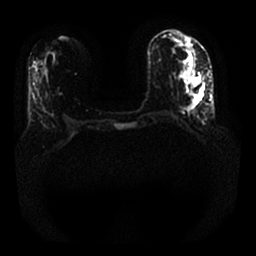
Breast MRI, one axial slice. Position 6 of 25 along the scan axis. Diffusion-weighted series; image 2 of 4 stored at this slice position (different b-values; order by instance number). 1.5 T. 256 × 256 image matrix, field of view 340 × 340 mm. Female patient.
Outlined on this slice (outlined manually by an expert reader):
- tumour on diffusion-weighted imaging: bounding box [x1, y1, x2, y2] px = [193, 87, 204, 103]